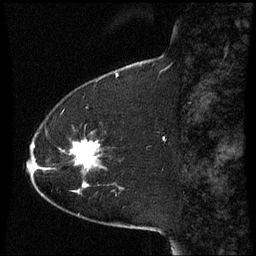
Breast MRI (dynamic contrast-enhanced), one sagittal slice; position 13 of 60 along the scan axis; dynamic contrast-enhanced series, image 2 of 3 at this slice position (ordered by acquisition); 1.5 T; TE 4.2 ms, TR 8.9 ms; 2.3 mm slice thickness; 256 × 256 image matrix, field of view 210 × 210 mm. Patient: female, 51 years. Case-level facts recorded for this patient, not image findings: setting: breast cancer imaged before/during neoadjuvant chemotherapy; receptor status: HR-positive, HER2-negative.
Outlined on this slice (semi-automatically segmented with operator editing):
- analysis volume of interest (the breast-tissue region the enhancement analysis was run in; not a lesion): bounding box (x1, y1, x2, y2) in pixels: (50, 142, 105, 187)
- tumour enhancement mask (voxels above the 70 % enhancement threshold inside the analysis volume of interest): (75, 142, 100, 168)